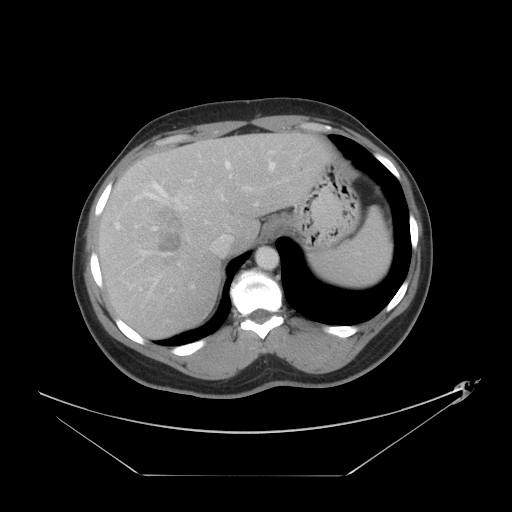
Contrast-enhanced abdominal CT, one axial slice; slice 32 of 44 in the series (ordered by position); intravenous contrast given; soft-tissue window (W 400 / L 40 HU); 512 × 512 image matrix, field of view 466 × 466 mm. Male patient, age 49 years. From the clinical record (not read from this slice): diagnosis: colorectal cancer liver metastases, imaged before liver resection; multiple liver metastases: no; largest metastasis: 8.5 cm; disease in both lobes: yes.
Outlined on this slice (outlined manually by an expert reader):
- hepatic veins: bounding box (x1, y1, x2, y2) in pixels: (136, 160, 276, 255)
- liver: (99, 133, 333, 338)
- planned liver remnant (the part of the liver to remain after resection): (191, 133, 333, 249)
- portal vein (with intrahepatic branches): (116, 160, 253, 291)
- liver metastasis: (157, 207, 185, 253)